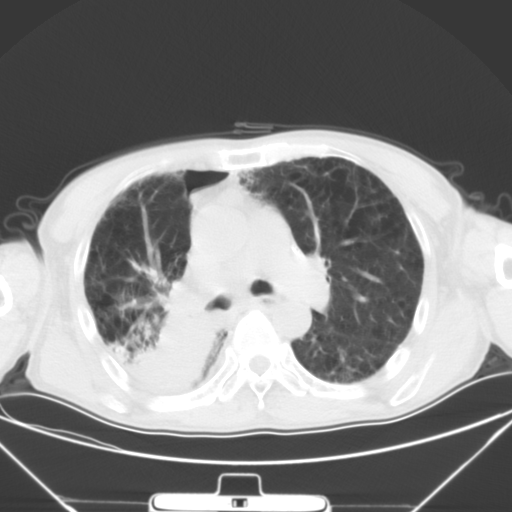
Chest CT, one axial slice; 120 kVp; lung window (W 1500 / L -600 HU); 512 × 512 image matrix, field of view 373 × 373 mm. Patient: male, 65 years. From the clinical record (not read from this slice): clinical TNM (as recorded): T3 N1 M1a.
Outlined on this slice (bounding box drawn by a radiologist):
- lung tumour (recorded histology: squamous cell carcinoma): box from (x=105, y=286) to (x=211, y=402) px